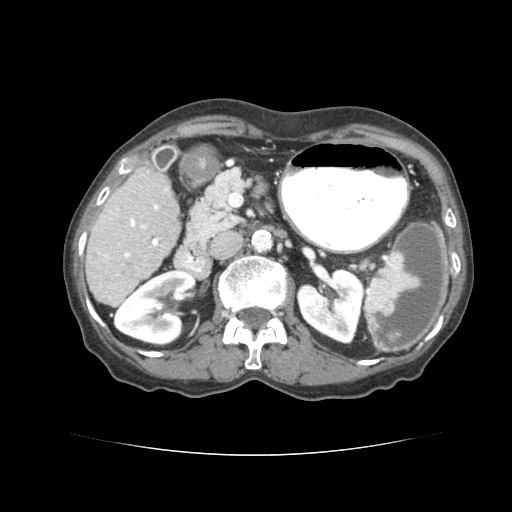
Contrast-enhanced abdominal CT (liver protocol), one axial slice; slice 30 of 77 in the series (ordered by position); reconstruction kernel STANDARD; 120 kVp; soft-tissue window (W 400 / L 40 HU); 2.5 mm slice thickness; 512 × 512 image matrix, field of view 340 × 340 mm. From the clinical record (not read from this slice): diagnosis: hepatocellular carcinoma (patient treated with transarterial chemoembolisation; whether this scan precedes or follows treatment is not stated here); TNM stage (as recorded): Stage-I; Child-Pugh class: A; tumour differentiation: well differentiated; tumour nodularity: uninodular.
Structures marked on this image (semi-automatic segmentation, software-assisted and operator-edited):
- liver parenchyma outside the tumour (the mass and vessels are separate outlines, so this box may not span the whole liver): bounding box <84,162,180,302> (left, top, right, bottom; pixels)
- liver vessels: <128,201,158,282>